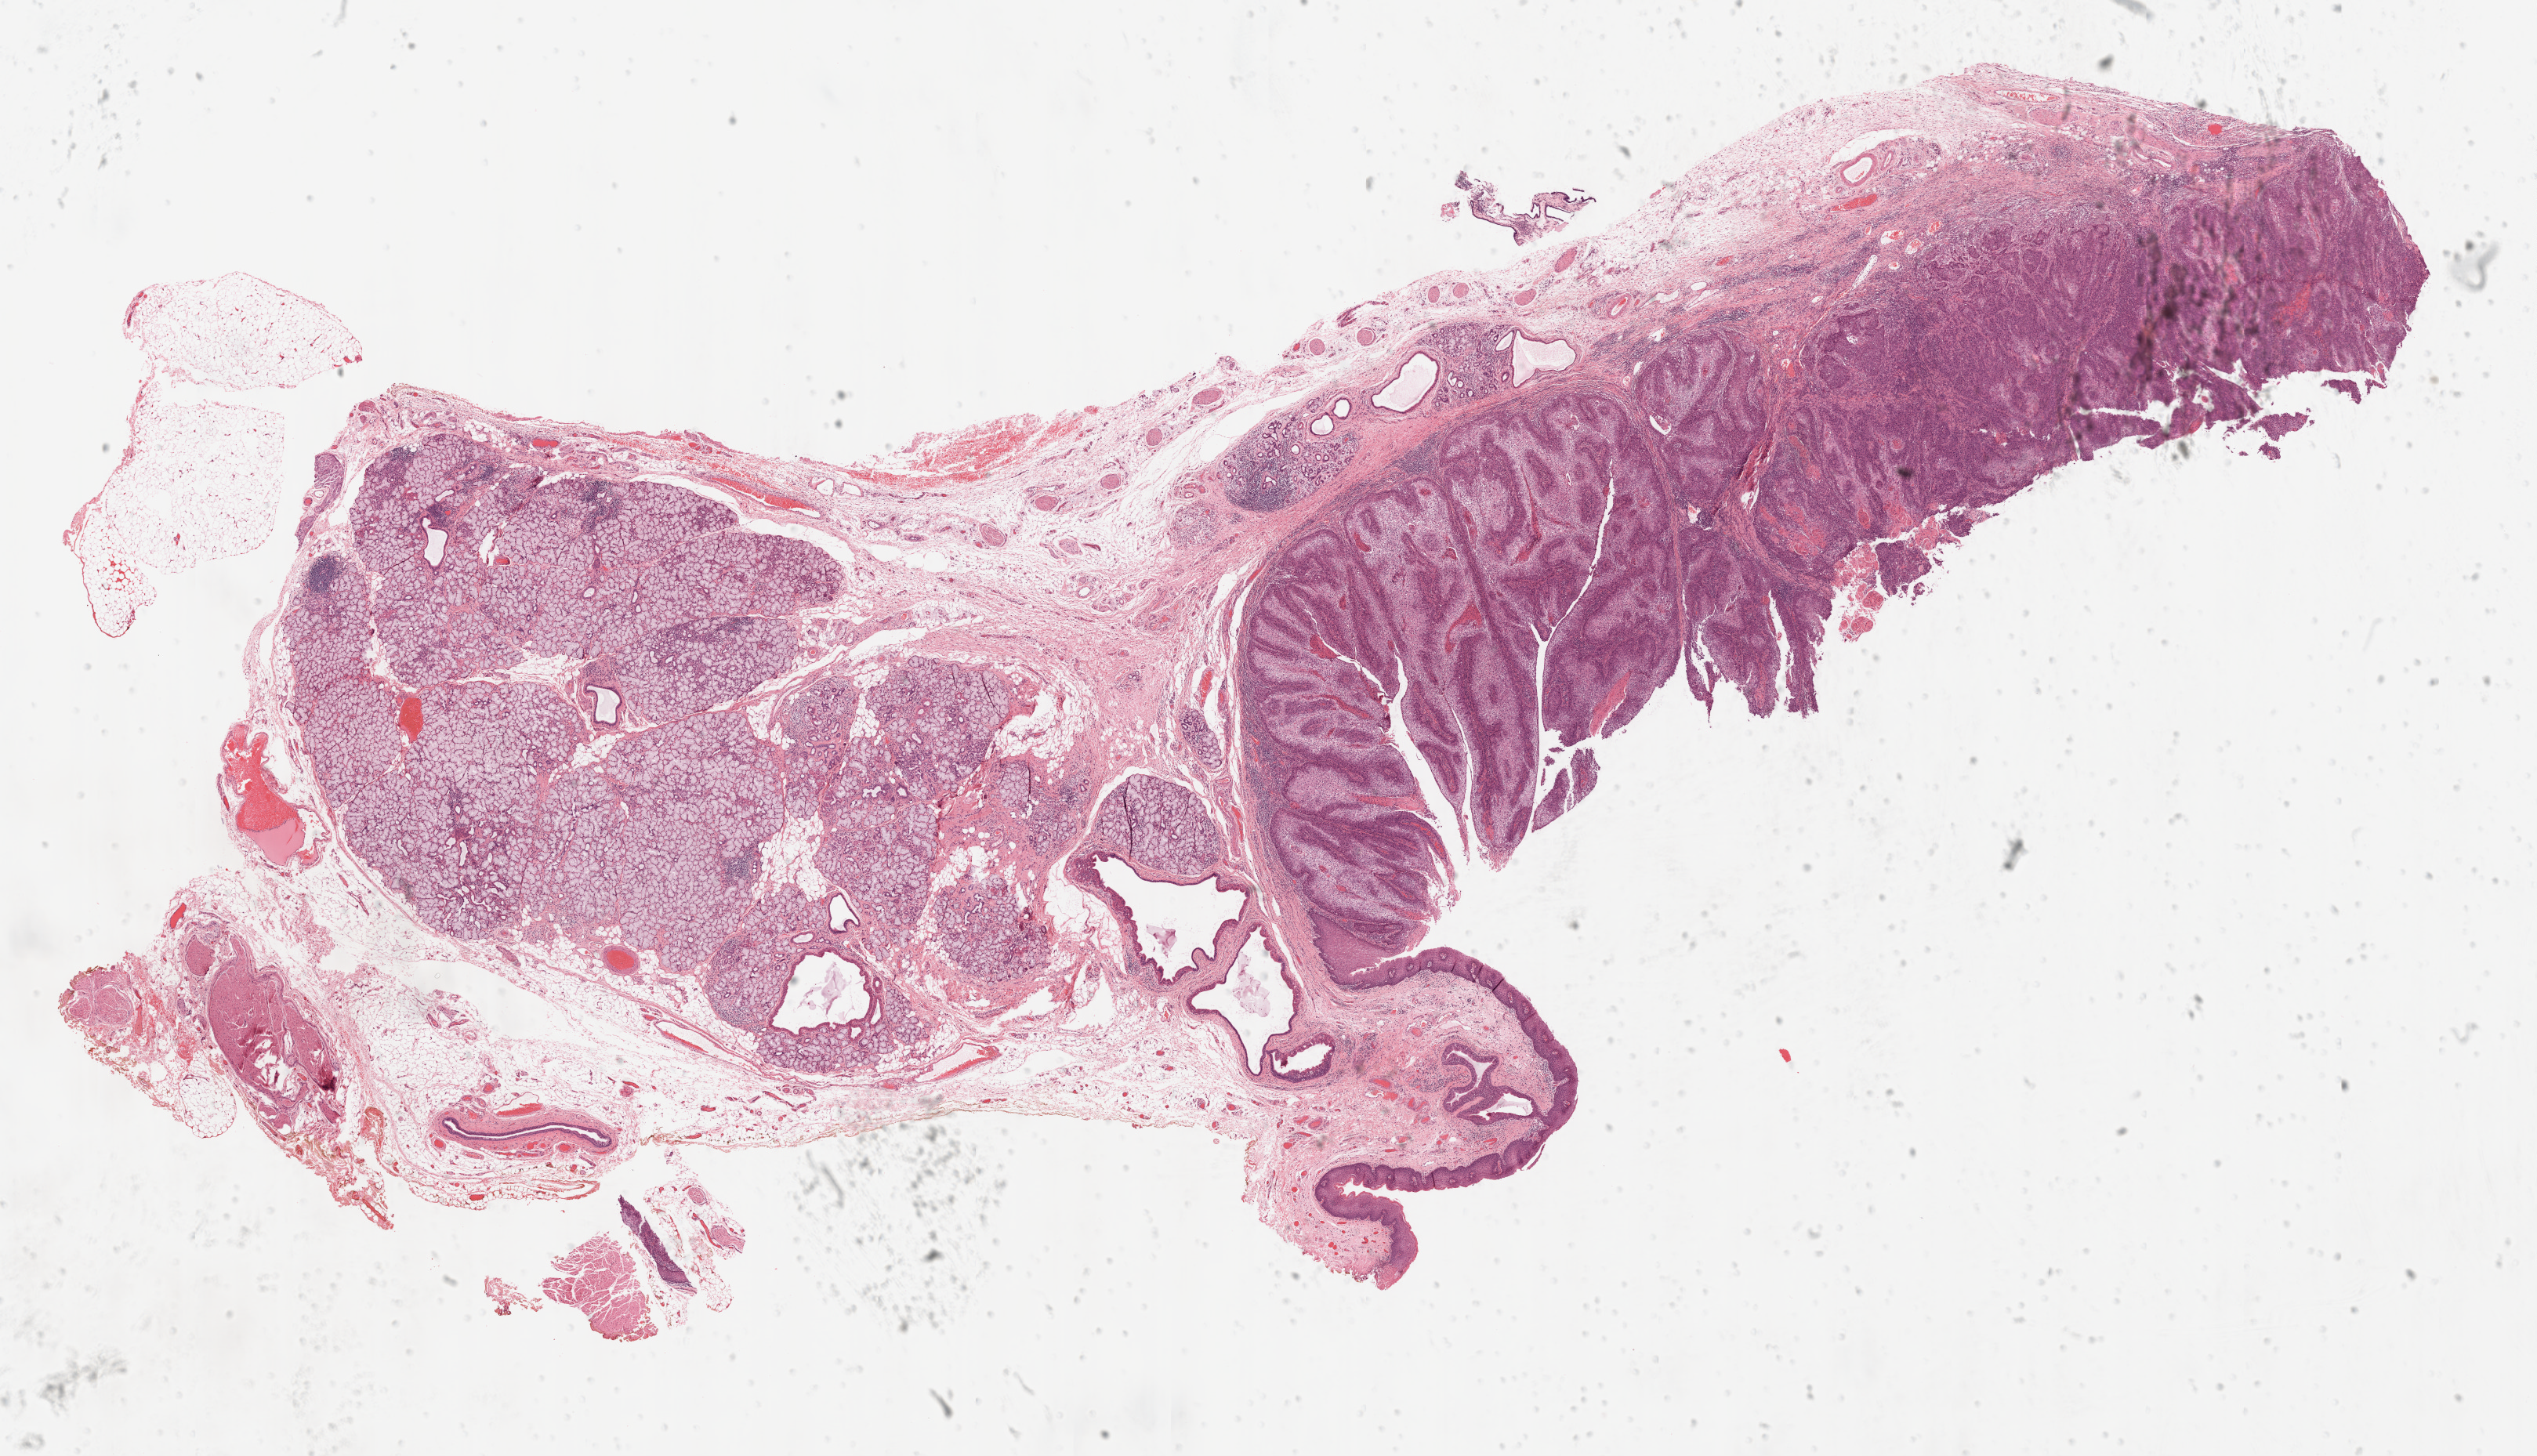
Hematoxylin and eosin (H&E) stained whole-slide image, whole scanned area (about 26.0 x 14.9 mm, from a 20x scan) shown as a low-resolution overview; formalin-fixed paraffin-embedded (FFPE) diagnostic section; head and neck, primary tumour sample. Female, age 80 years at initial diagnosis. Histologic grade: G2 (moderately differentiated).
* laterality: right
* AJCC pathologic stage: II
* diagnosis: Squamous cell carcinoma, NOS (overlapping lesion of lip, oral cavity and pharynx)